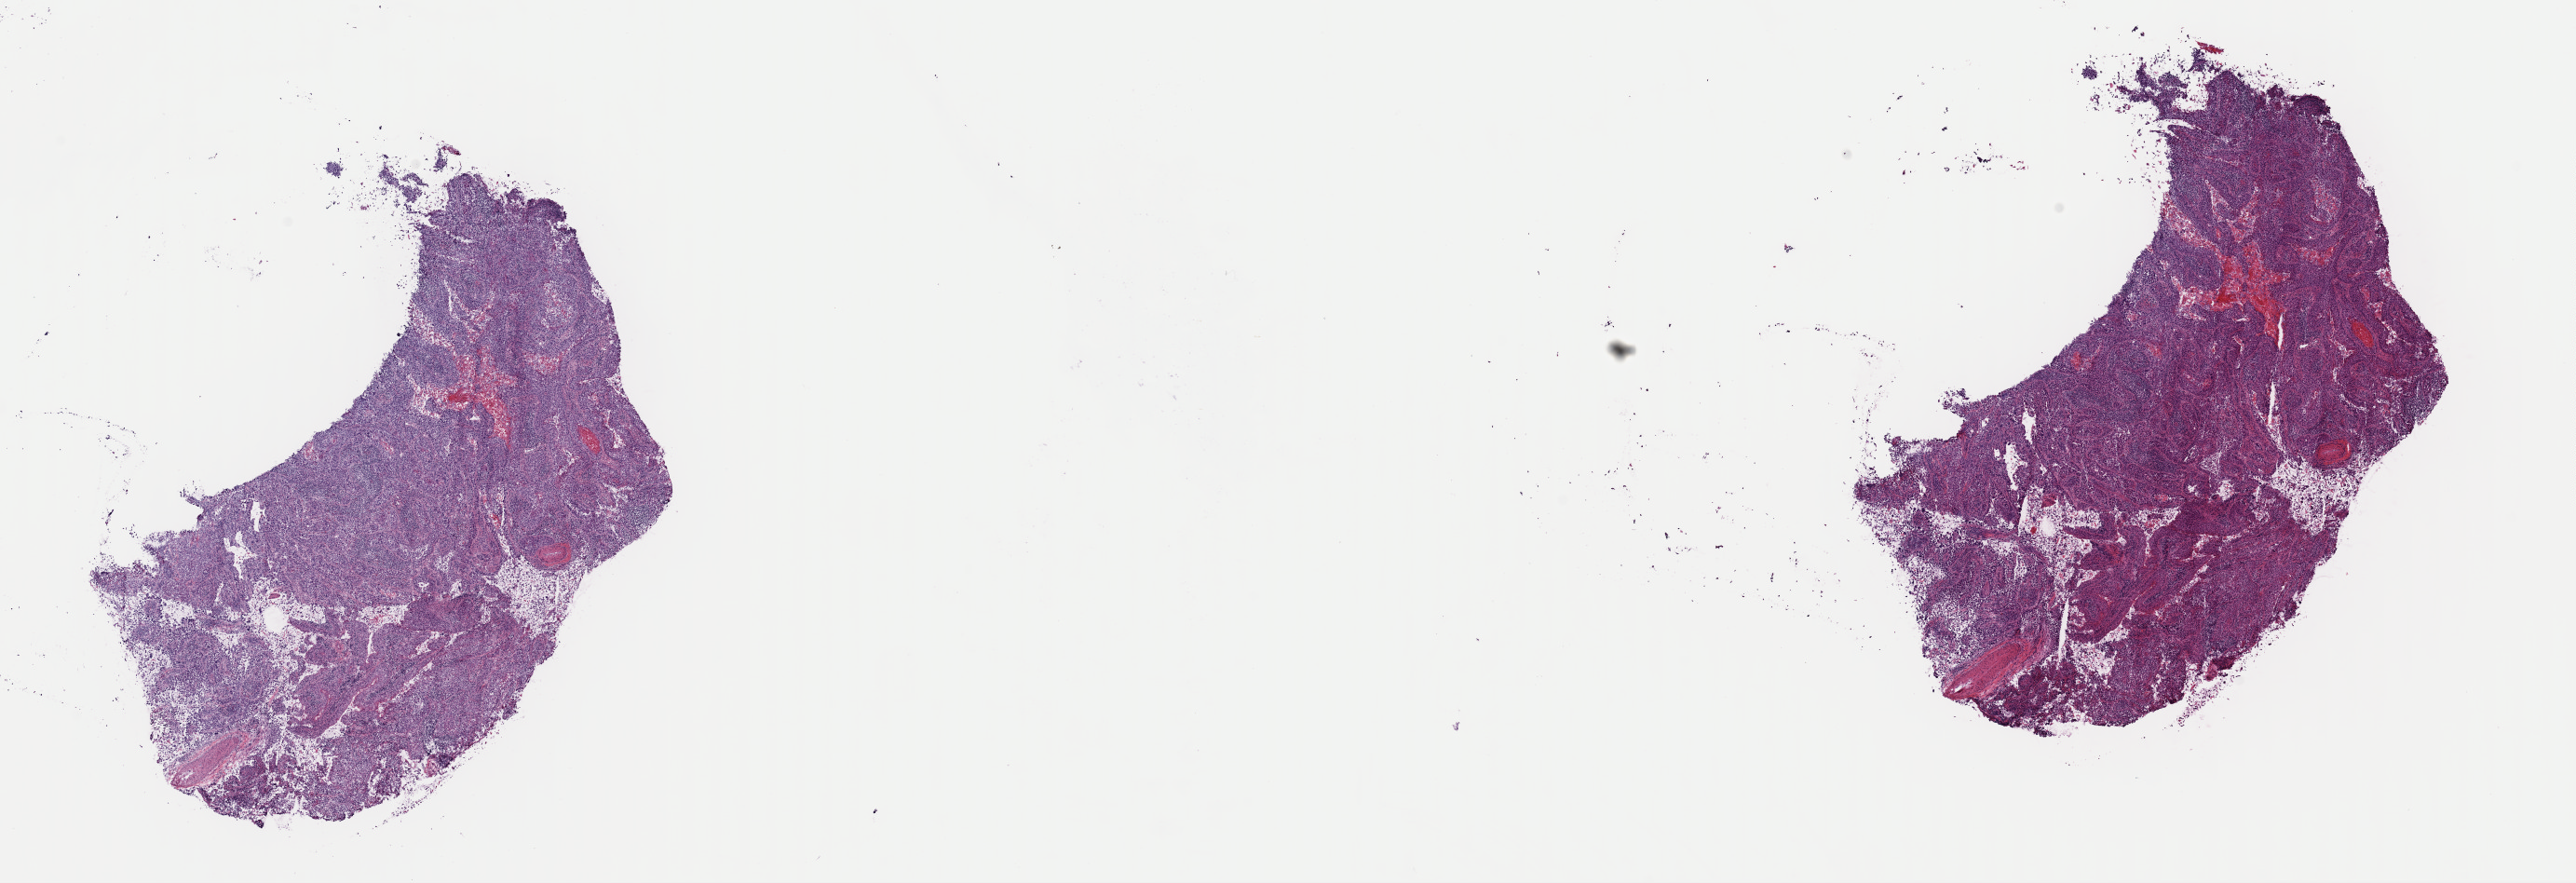
Hematoxylin and eosin (H&E) stained whole-slide image, a low-resolution overview of the entire scanned area, about 21.9 x 7.5 mm (acquisition: 40x scan); frozen section from the top of the tissue portion; primary tumour sample from the cervix. Patient: female, age at initial diagnosis 34 years. Histologic grade: GX (grade cannot be assessed). Composition of this section per pathologist review: tumour cells 85%, tumour nuclei 85%, normal cells 0%, stromal cells 5%, necrosis 10%. Inflammatory infiltration, as recorded: lymphocyte infiltration 40%, monocyte infiltration 20%, neutrophil infiltration 20%.
• pathologic diagnosis: Squamous cell carcinoma, NOS (cervix uteri)
• FIGO stage: IIB